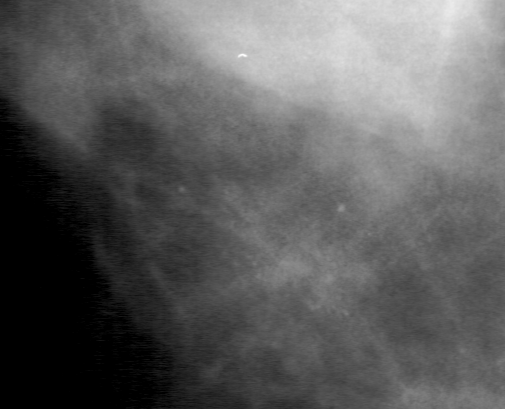
Region of interest cut from a scanned film mammogram (one marked finding), left breast, CC view, BI-RADS breast density category 4 (scale 1–4).
Finding: calcifications, morphology amorphous, distribution clustered; BI-RADS assessment category 4; subtlety rating 3 on a 1 (subtle) to 5 (obvious) scale; pathology (as recorded): benign.